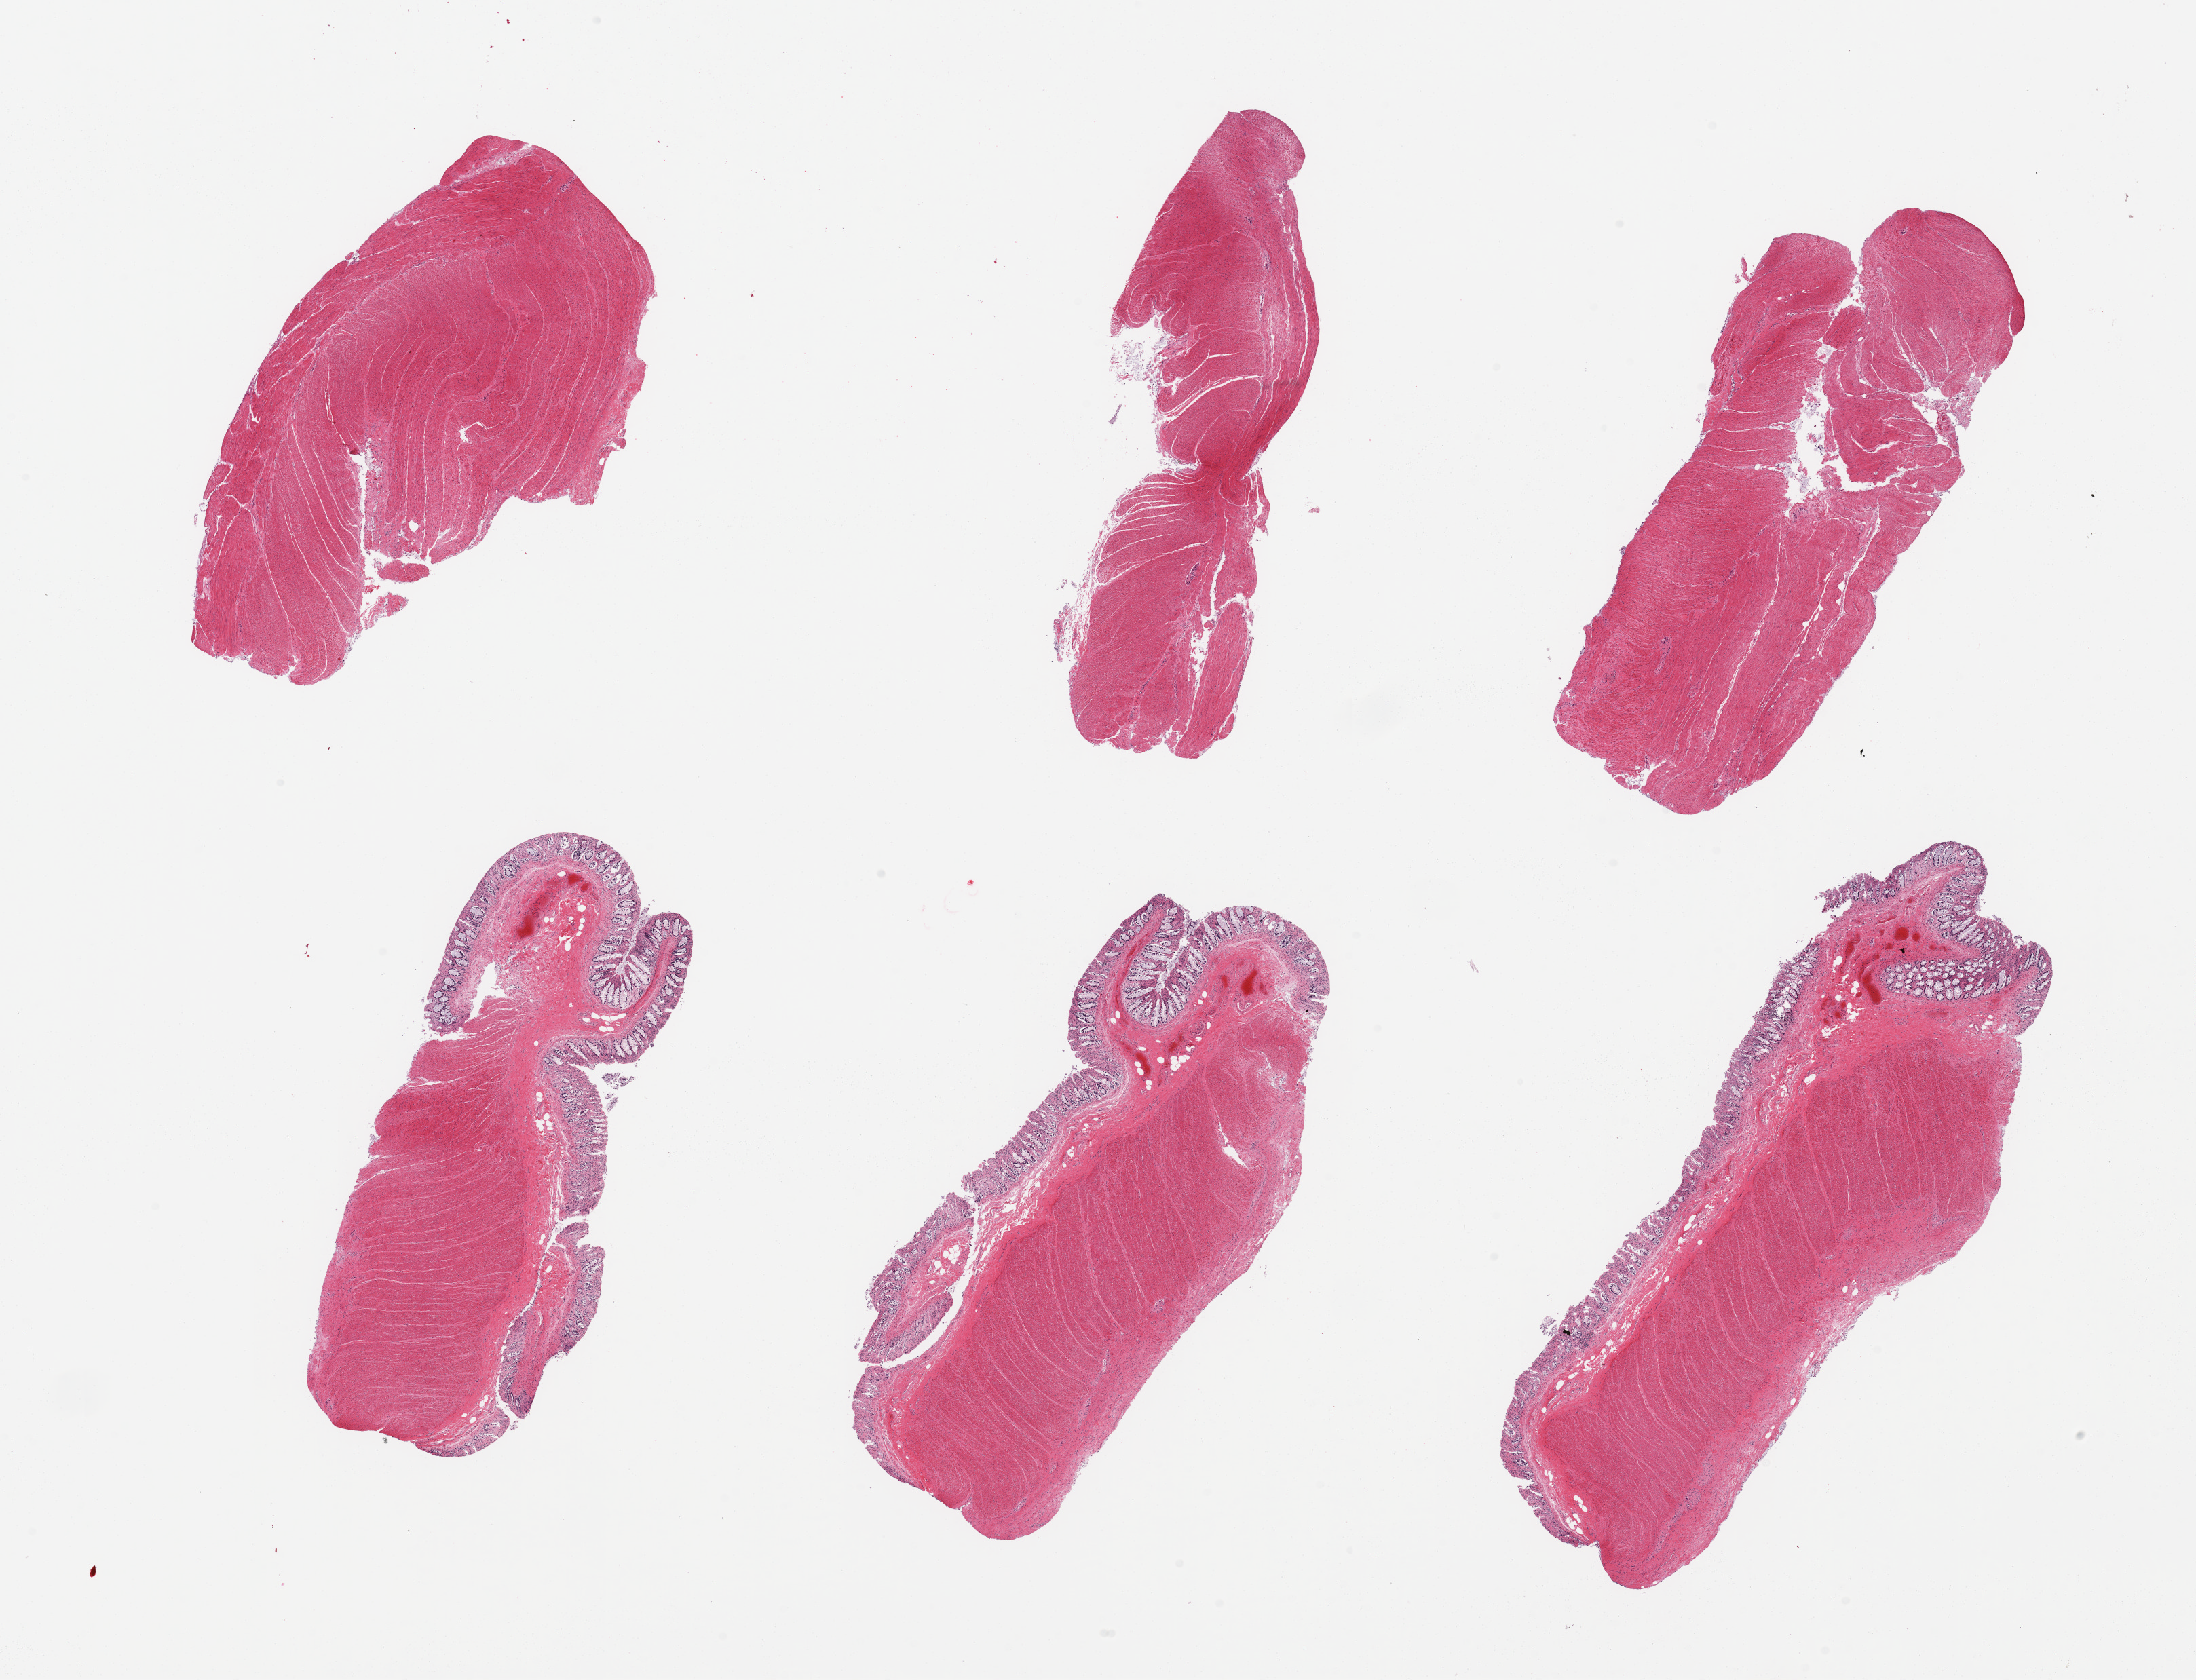
Whole-slide image, haematoxylin and eosin stain — a low-resolution overview of the entire scanned area, about 25.6 x 19.6 mm (slide scanned at 20x); PAXgene-fixed paraffin-embedded (PFPE) section; target tissue: sigmoid colon; tissue donor sample. Donor: male.
Pathologist's review note for this sample: 6 pieces; three are full thickness (mucosa not target).